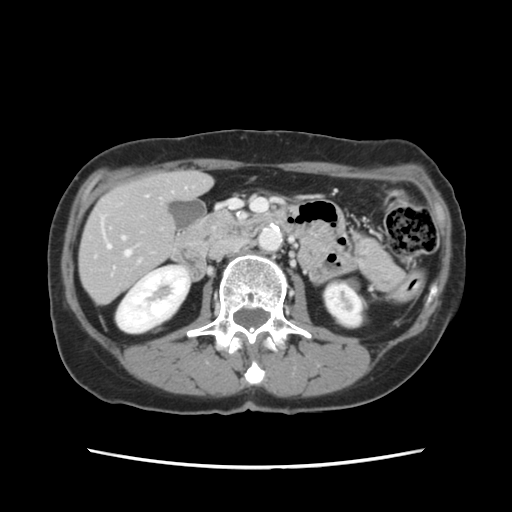
Contrast-enhanced abdominal CT, one axial slice; position 43 of 120 along the scan axis; intravenous contrast given; soft-tissue window (W 400 / L 40 HU); 2.5 mm slice thickness; 512 × 512 image matrix, field of view 330 × 330 mm. Female patient, age 70 years. From the clinical record (not read from this slice): diagnosis: colorectal cancer liver metastases, imaged before liver resection; multiple liver metastases: no; largest metastasis: 2.5 cm; disease in both lobes: no.
Annotated regions visible in this slice (manually delineated by an expert):
- hepatic veins: box from (x=107, y=244) to (x=131, y=256) px
- liver: (x=80, y=172)–(x=210, y=303)
- planned liver remnant (the part of the liver to remain after resection): (x=80, y=172)–(x=210, y=303)
- portal vein (with intrahepatic branches): (x=122, y=236)–(x=125, y=240)